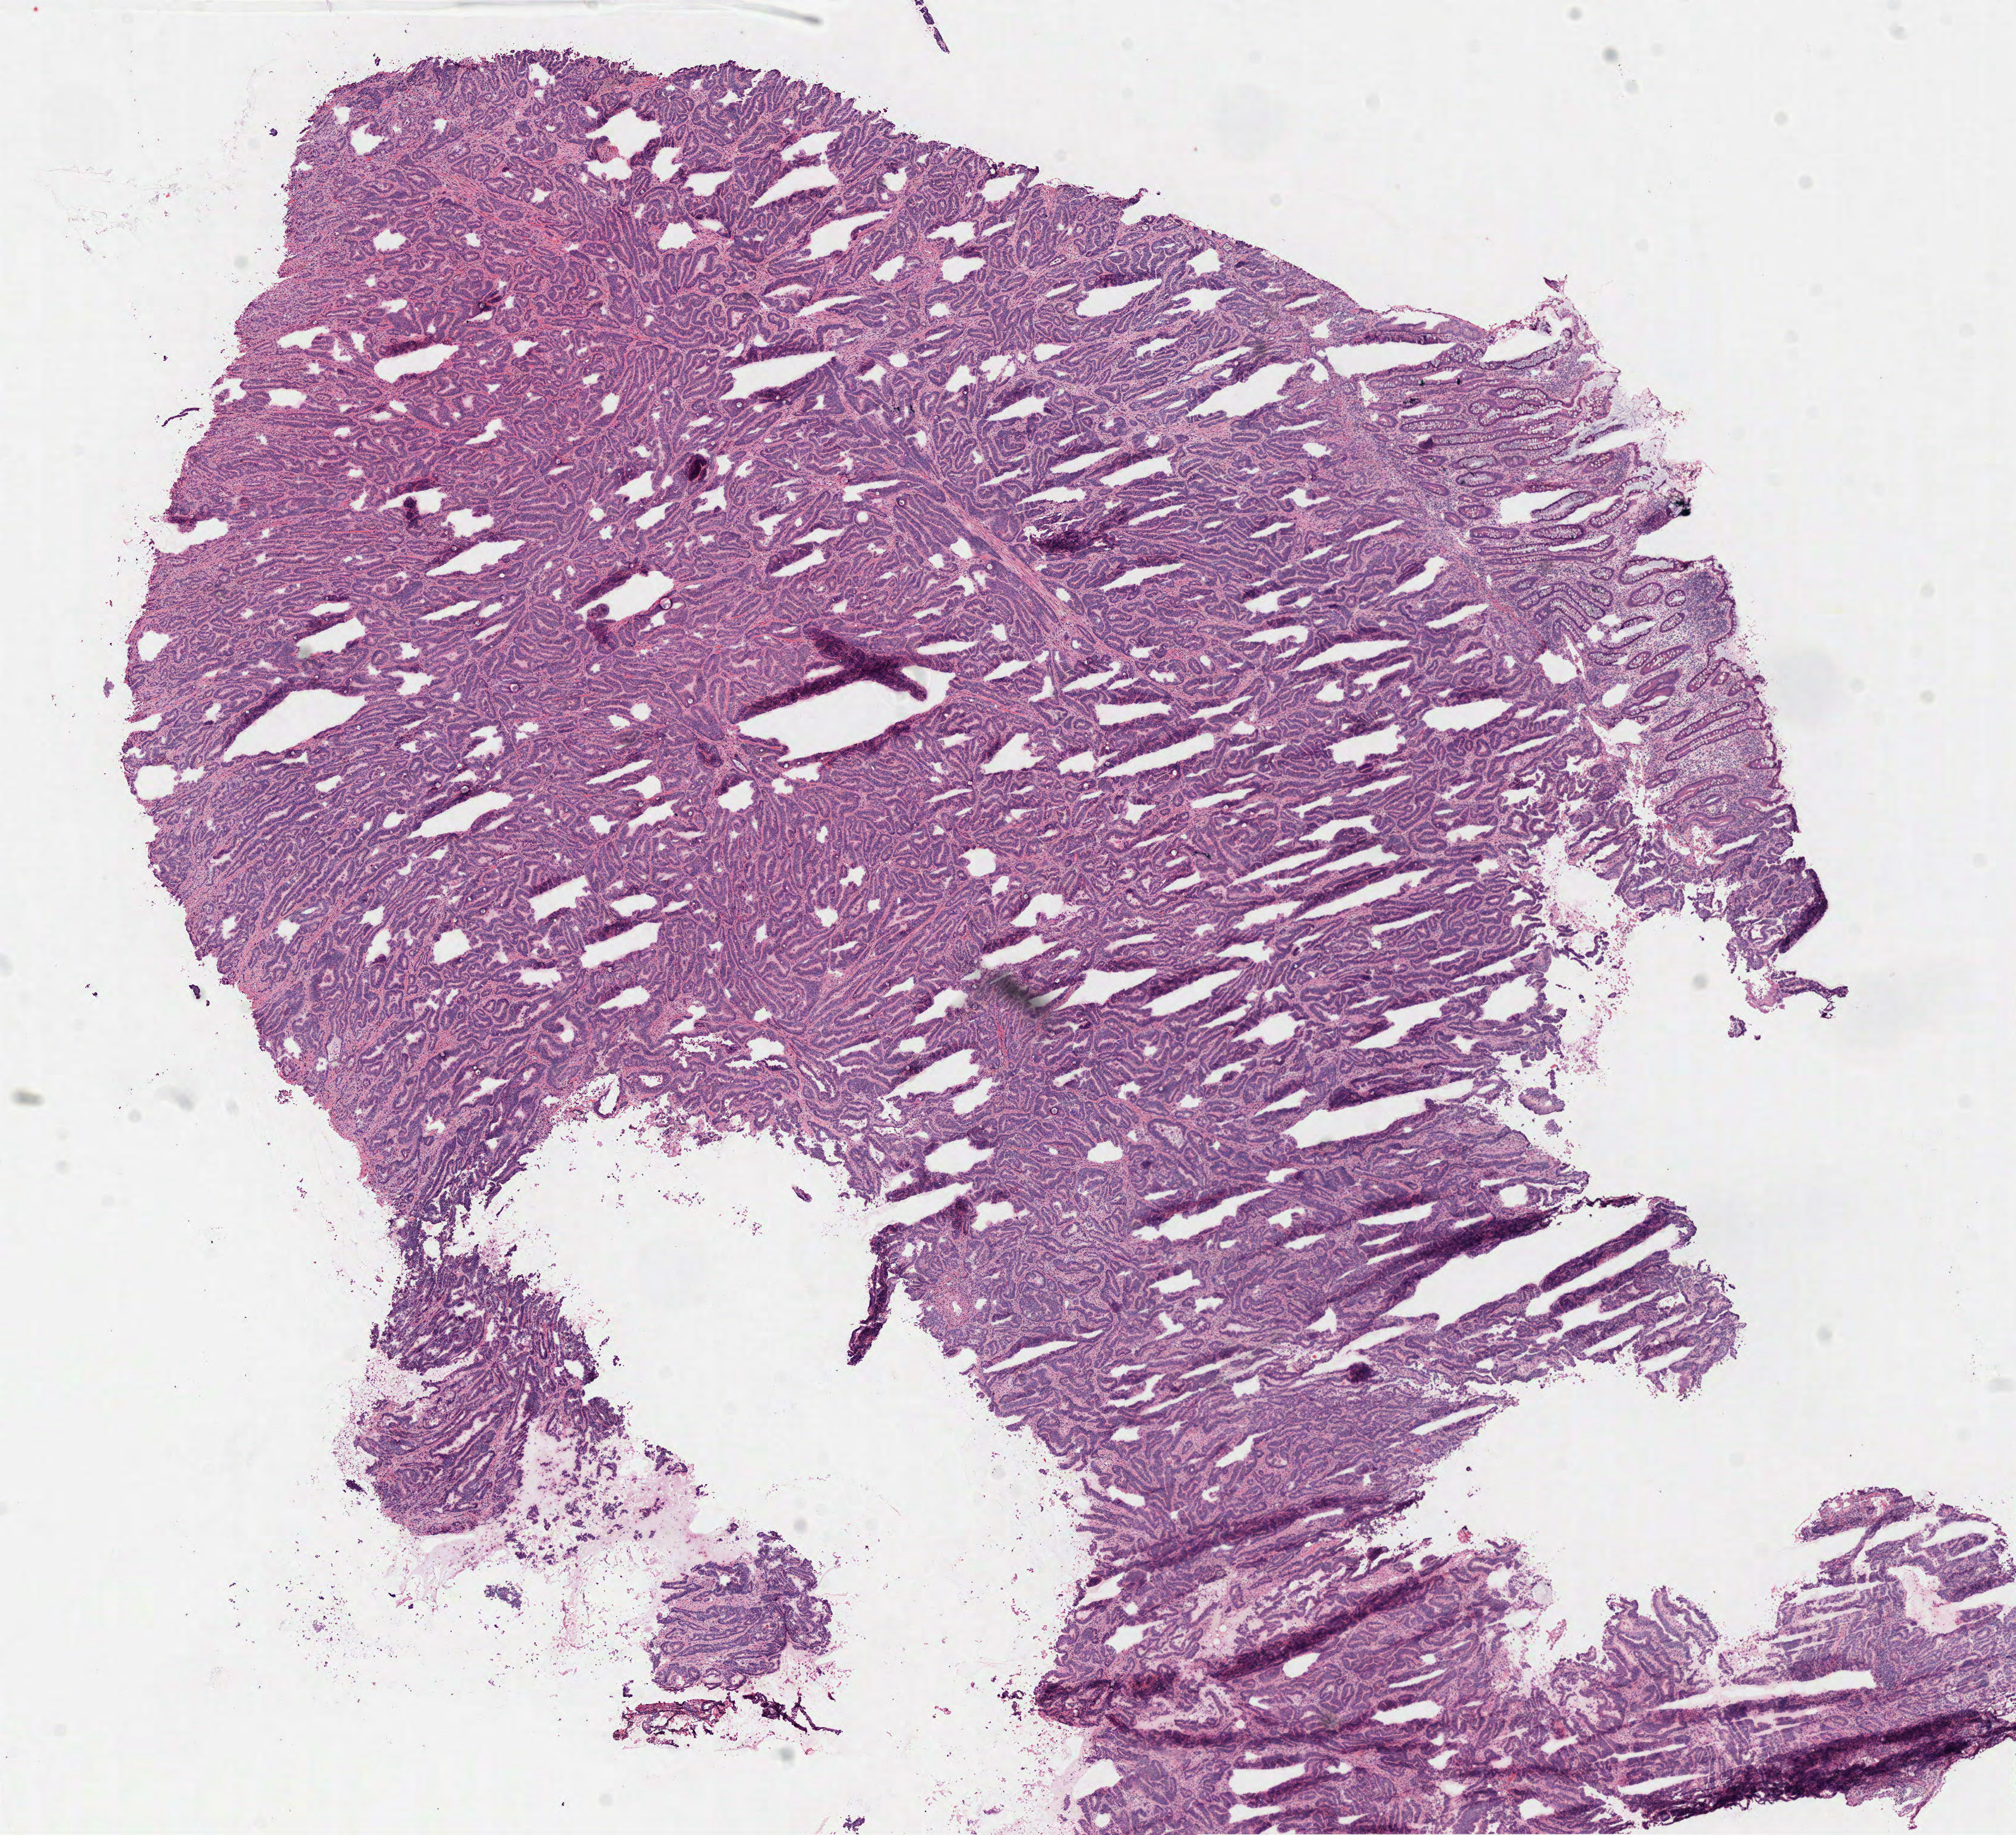
Whole-slide histology image, Hematoxylin and eosin (H&E) stained, whole scanned area (about 13.6 x 12.3 mm, acquisition: 40x scan) shown as a low-resolution overview; frozen section from the top of the tissue portion; sample: primary tumour, colon. Male, age 35 years at initial diagnosis. Pathologist review of this section (percent, as recorded): tumour cells 80%, tumour nuclei 85%, normal cells 5%, stromal cells 10%, necrosis 5%.
* lymph nodes positive (case pathology): 12 of 72 examined
* AJCC pathologic stage: IVB (7th edition)
* pathologic diagnosis: Adenocarcinoma, NOS (cecum)